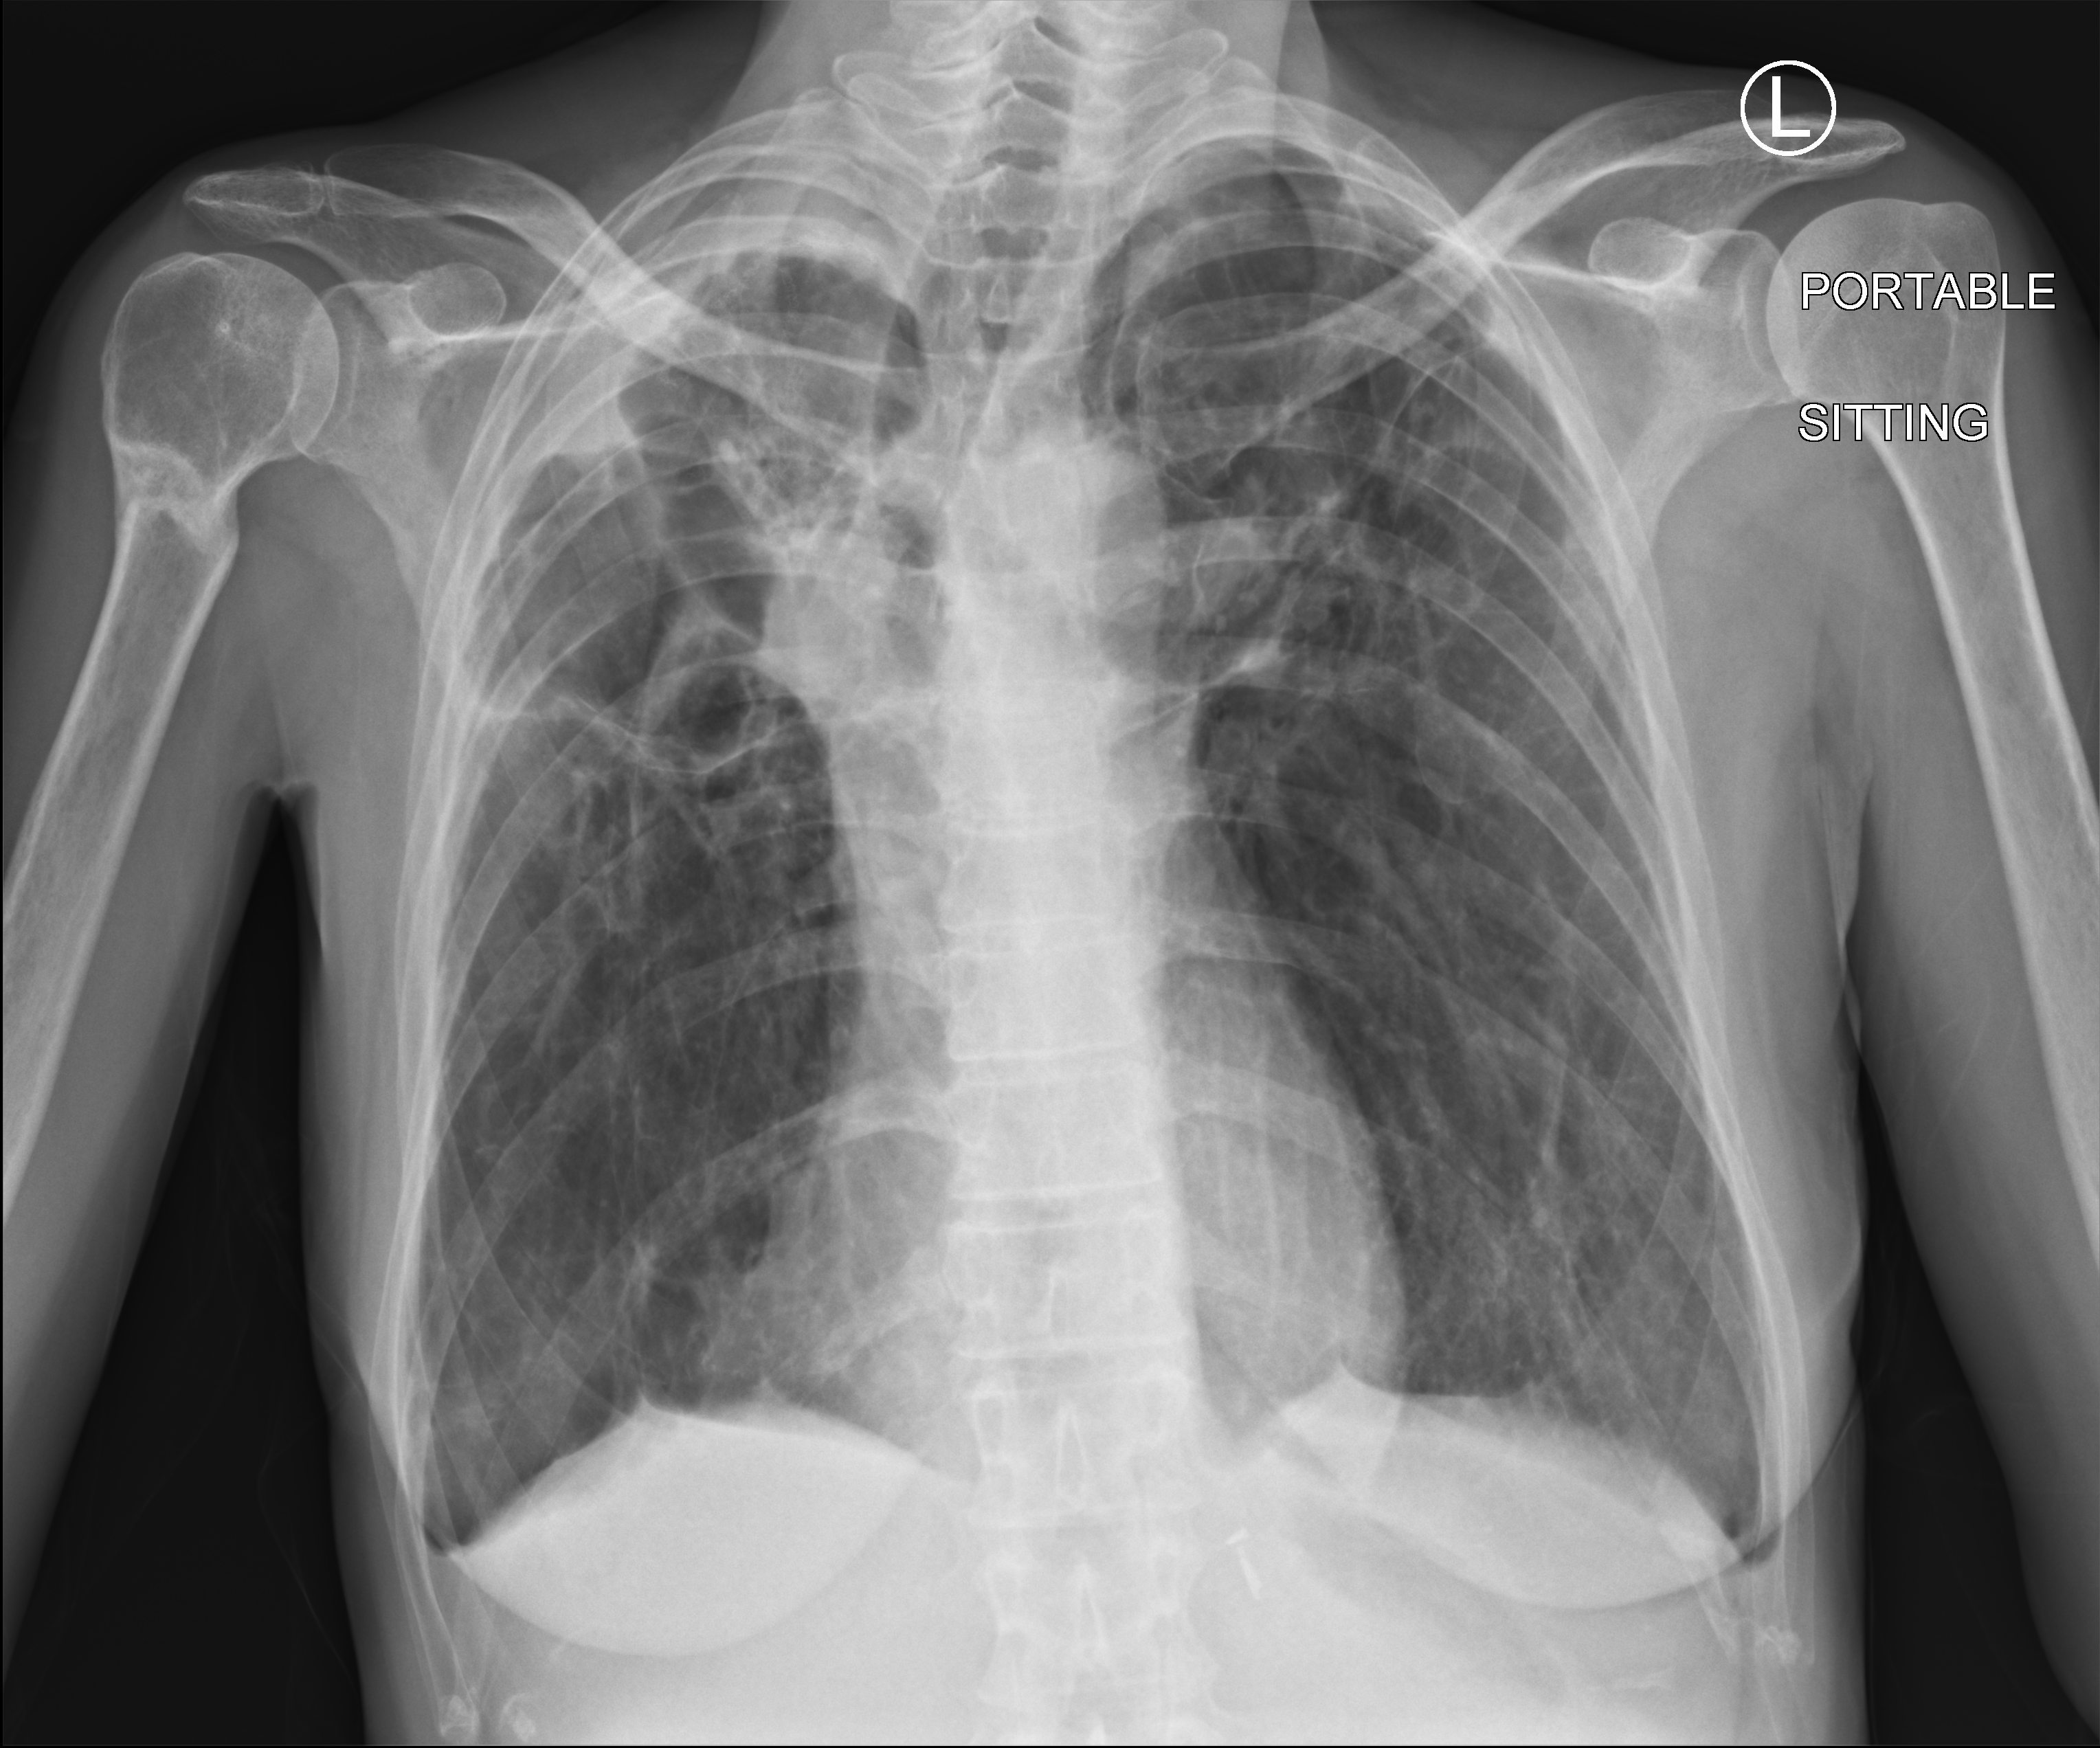
Chest X-ray (portable), anteroposterior (AP) projection. Patient hospitalised with COVID-19; female, aged 18–59 years.
Hospital-stay facts (about this admission, not read from this image; timing relative to this image not recorded): smoking status (admission record): former; admitted to intensive care during this hospital stay: no.